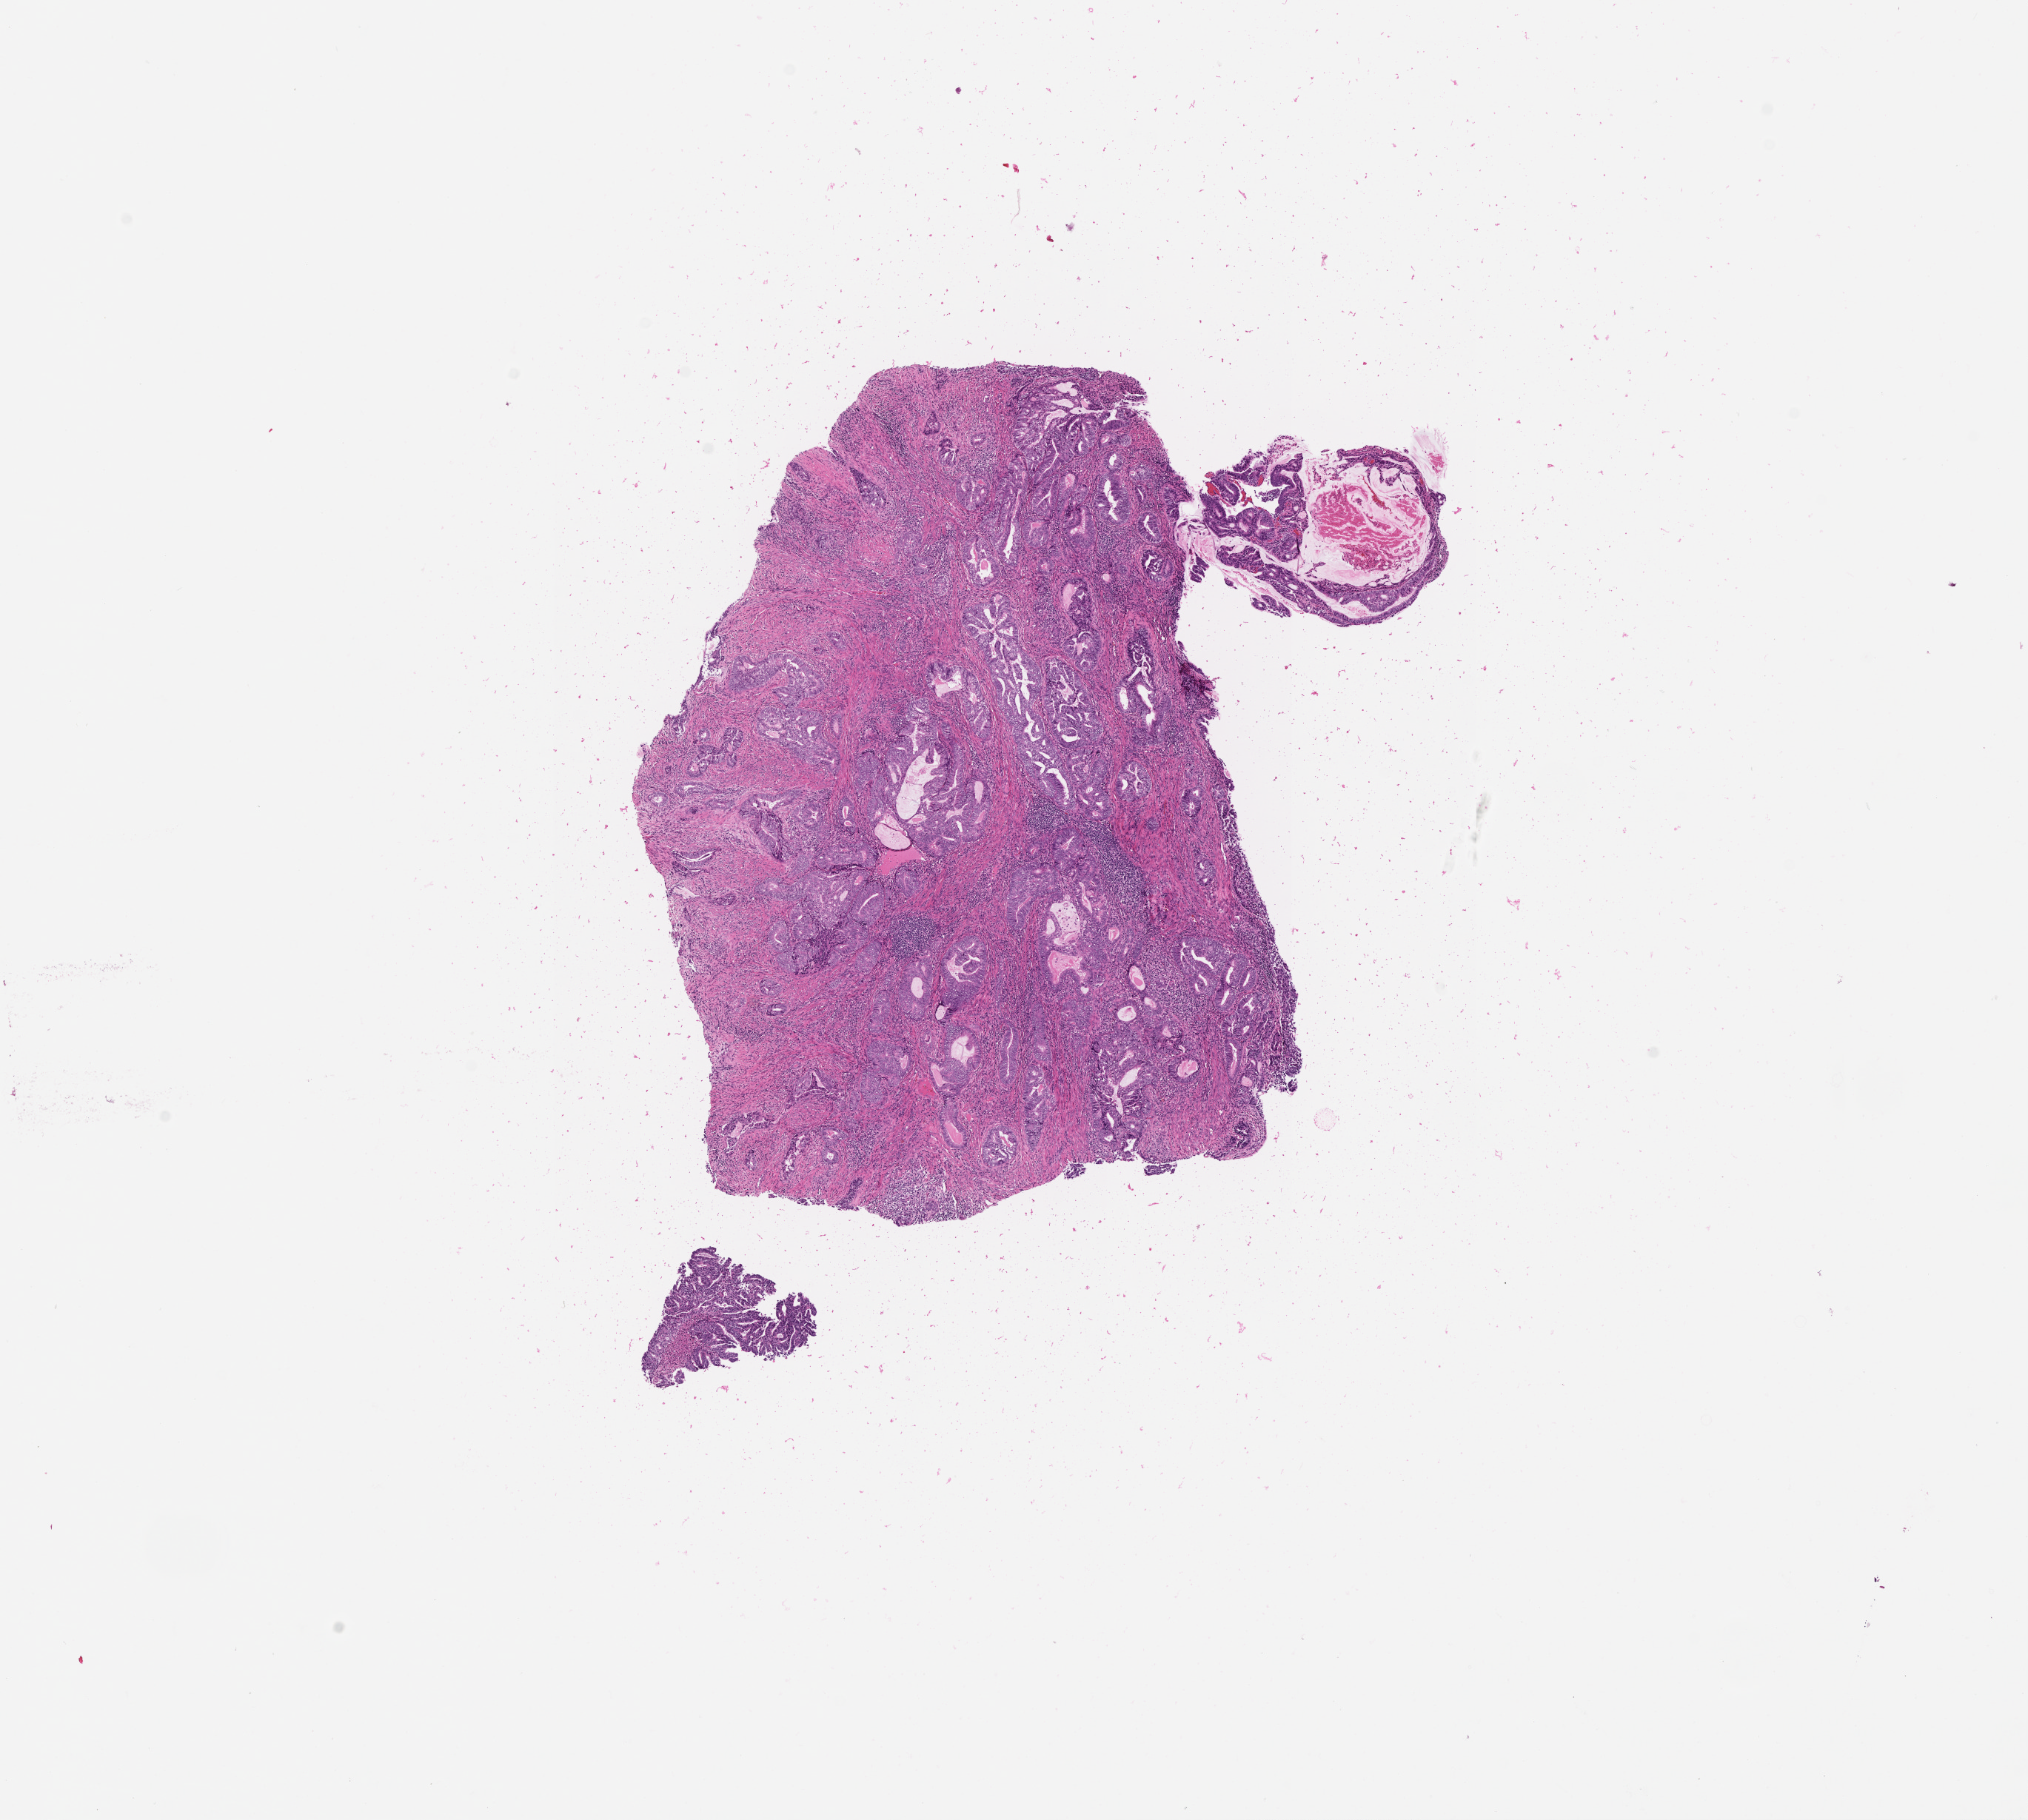
Digitized Hematoxylin and eosin (H&E) stained tissue section (whole slide) — whole scanned area (about 11.0 x 9.9 mm) shown as a low-resolution overview, uterus, tumour tissue. Patient: female, age 68 years. Histologic grade: G2 (moderately differentiated).
Histologic diagnosis: Endometrioid adenocarcinoma, NOS.